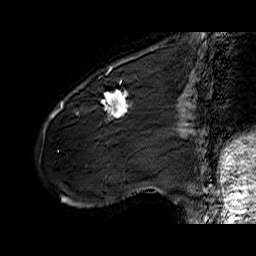
Breast MRI (dynamic contrast-enhanced), one sagittal slice; slice 17 of 60 in the series (ordered by position); dynamic contrast-enhanced series, time point 2 of 6 at this slice position (early post-contrast); 1.5 T; TE 6.4 ms, TR 32.9 ms; 256 × 256 image matrix, field of view 200 × 200 mm. Female patient. From the clinical record (not read from this slice): setting: breast cancer imaged before/during neoadjuvant chemotherapy; receptor status: HER2-positive.
Structures marked on this image (semi-automatic segmentation, software-assisted and operator-edited):
- analysis volume of interest (the breast-tissue region the enhancement analysis was run in; not a lesion): bounding box [x1, y1, x2, y2] px = [61, 77, 141, 142]
- tumour enhancement mask (voxels above the 100 % enhancement threshold inside the analysis volume of interest): [61, 89, 132, 120]